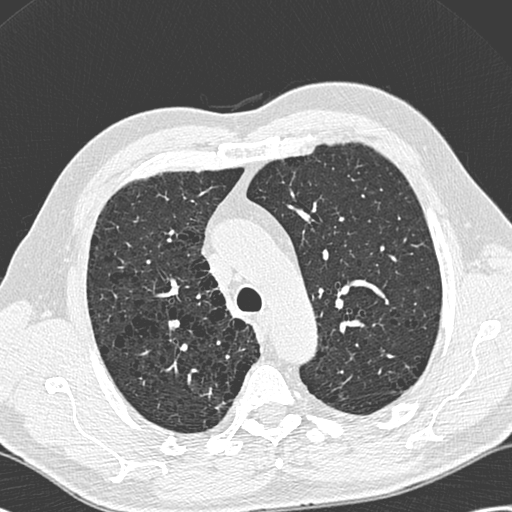
Axial slice from a low-dose chest CT screening exam. Baseline screening round. Lung window (W 1500 / L -600 HU). Lung (sharp) reconstruction kernel (D). Slice 66 of 258 in the series. 512 × 512 image matrix, field of view 358 × 358 mm. Male, age 68 years at enrolment.
Lesion marked by an expert reader, bounding box (x1, y1, x2, y2) in pixels: (203, 391, 245, 422). No non-calcified nodule or mass ≥4 mm was recorded by the screening reader at this exam. Participant outcome: lung cancer diagnosed 777 days after this screen (after the third annual screen) — adenocarcinoma, NOS, right upper lobe, well differentiated (G1), stage IB (AJCC 6th edition), 15 mm at pathology.